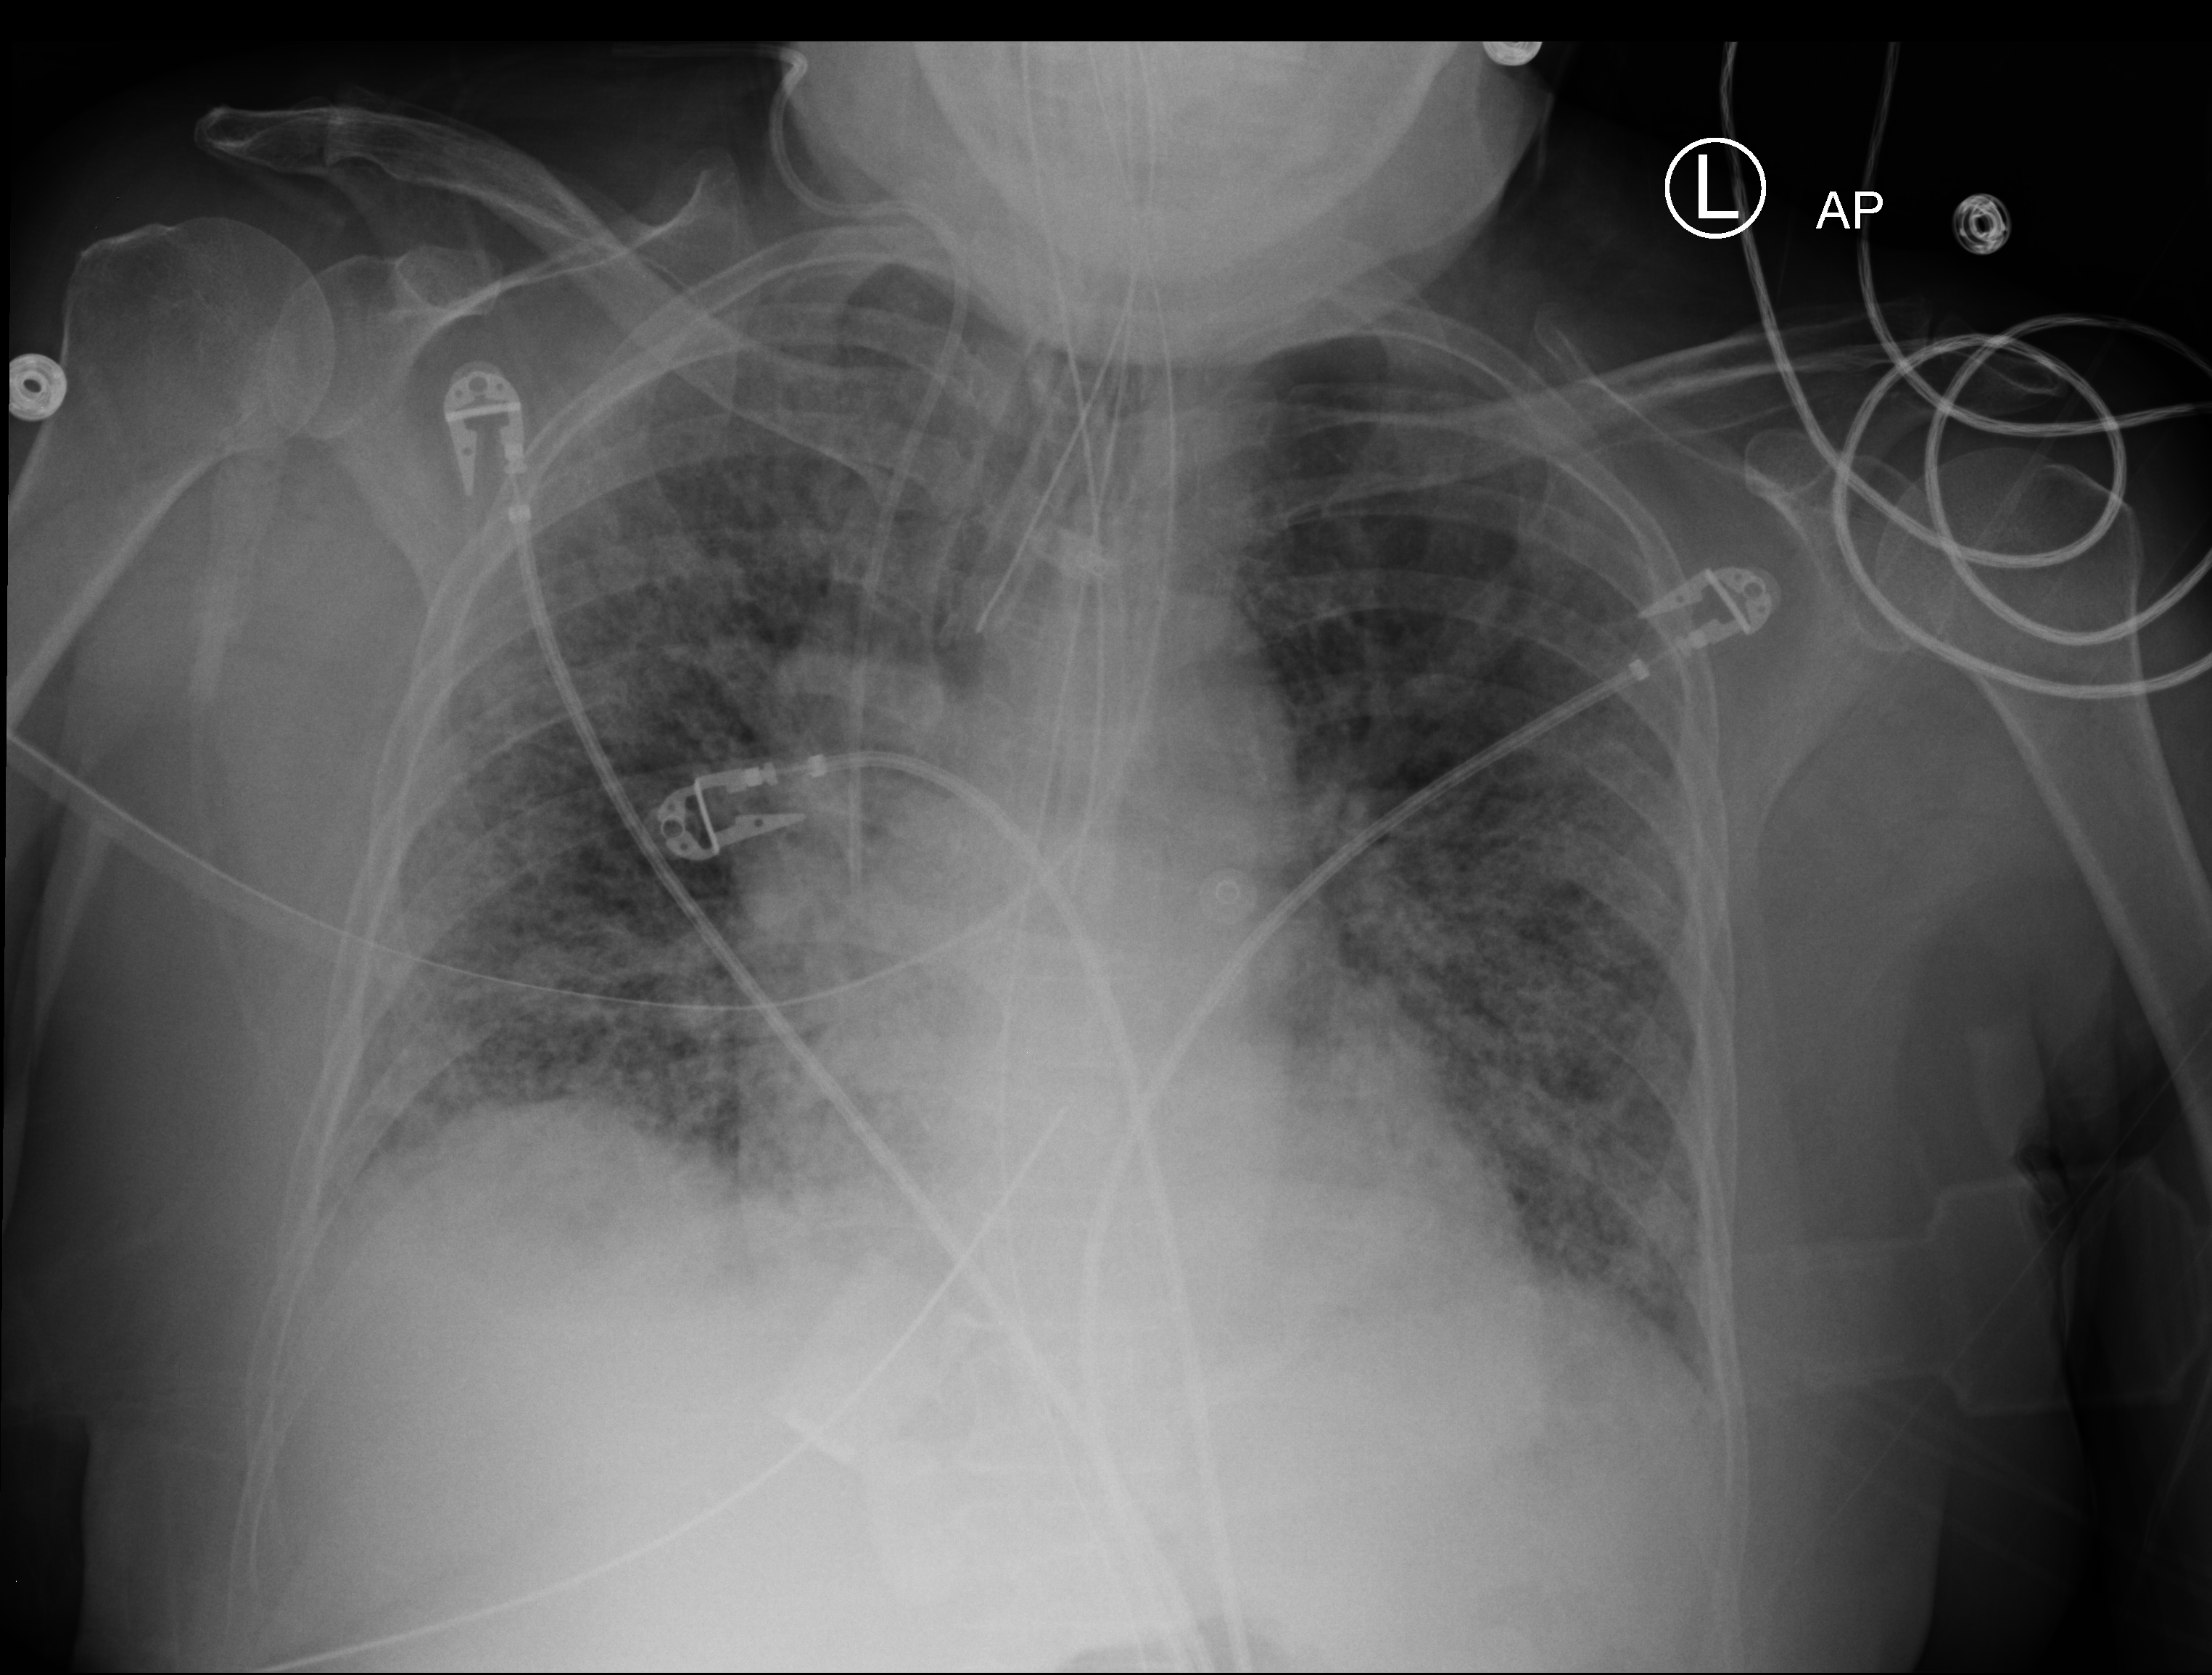
Bedside chest radiograph (computed radiography); anteroposterior (AP) projection. Patient hospitalised with COVID-19; female, aged 60–74 years.
Hospital-stay facts (about this admission, not read from this image; timing relative to this image not recorded): other chronic lung disease (admission record): yes; admitted to intensive care during this hospital stay: yes.